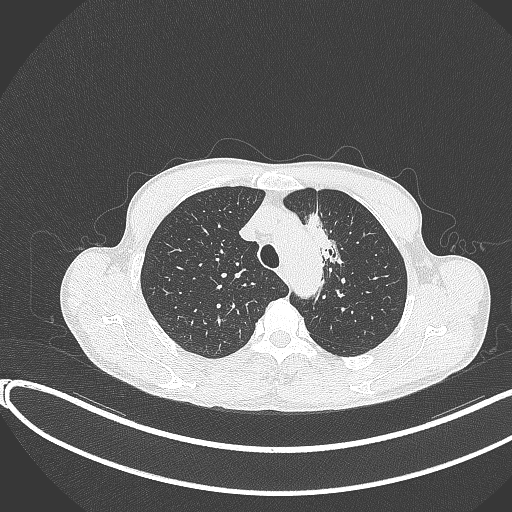
Chest CT, one axial slice. Slice 297 of 374 in the series (ordered by position). Reconstruction kernel B70f. 120 kVp. Lung window (W 1500 / L -600 HU). 1 mm slice thickness. 512 × 512 image matrix, field of view 400 × 400 mm. Male patient, age 58 years. Case-level facts recorded for this patient, not image findings: clinical TNM (as recorded): T1c N1 M0.
Outlined on this slice (bounding box drawn by a radiologist):
- lung tumour (recorded histology: adenocarcinoma): bounding box <303,210,344,271> (left, top, right, bottom; pixels)